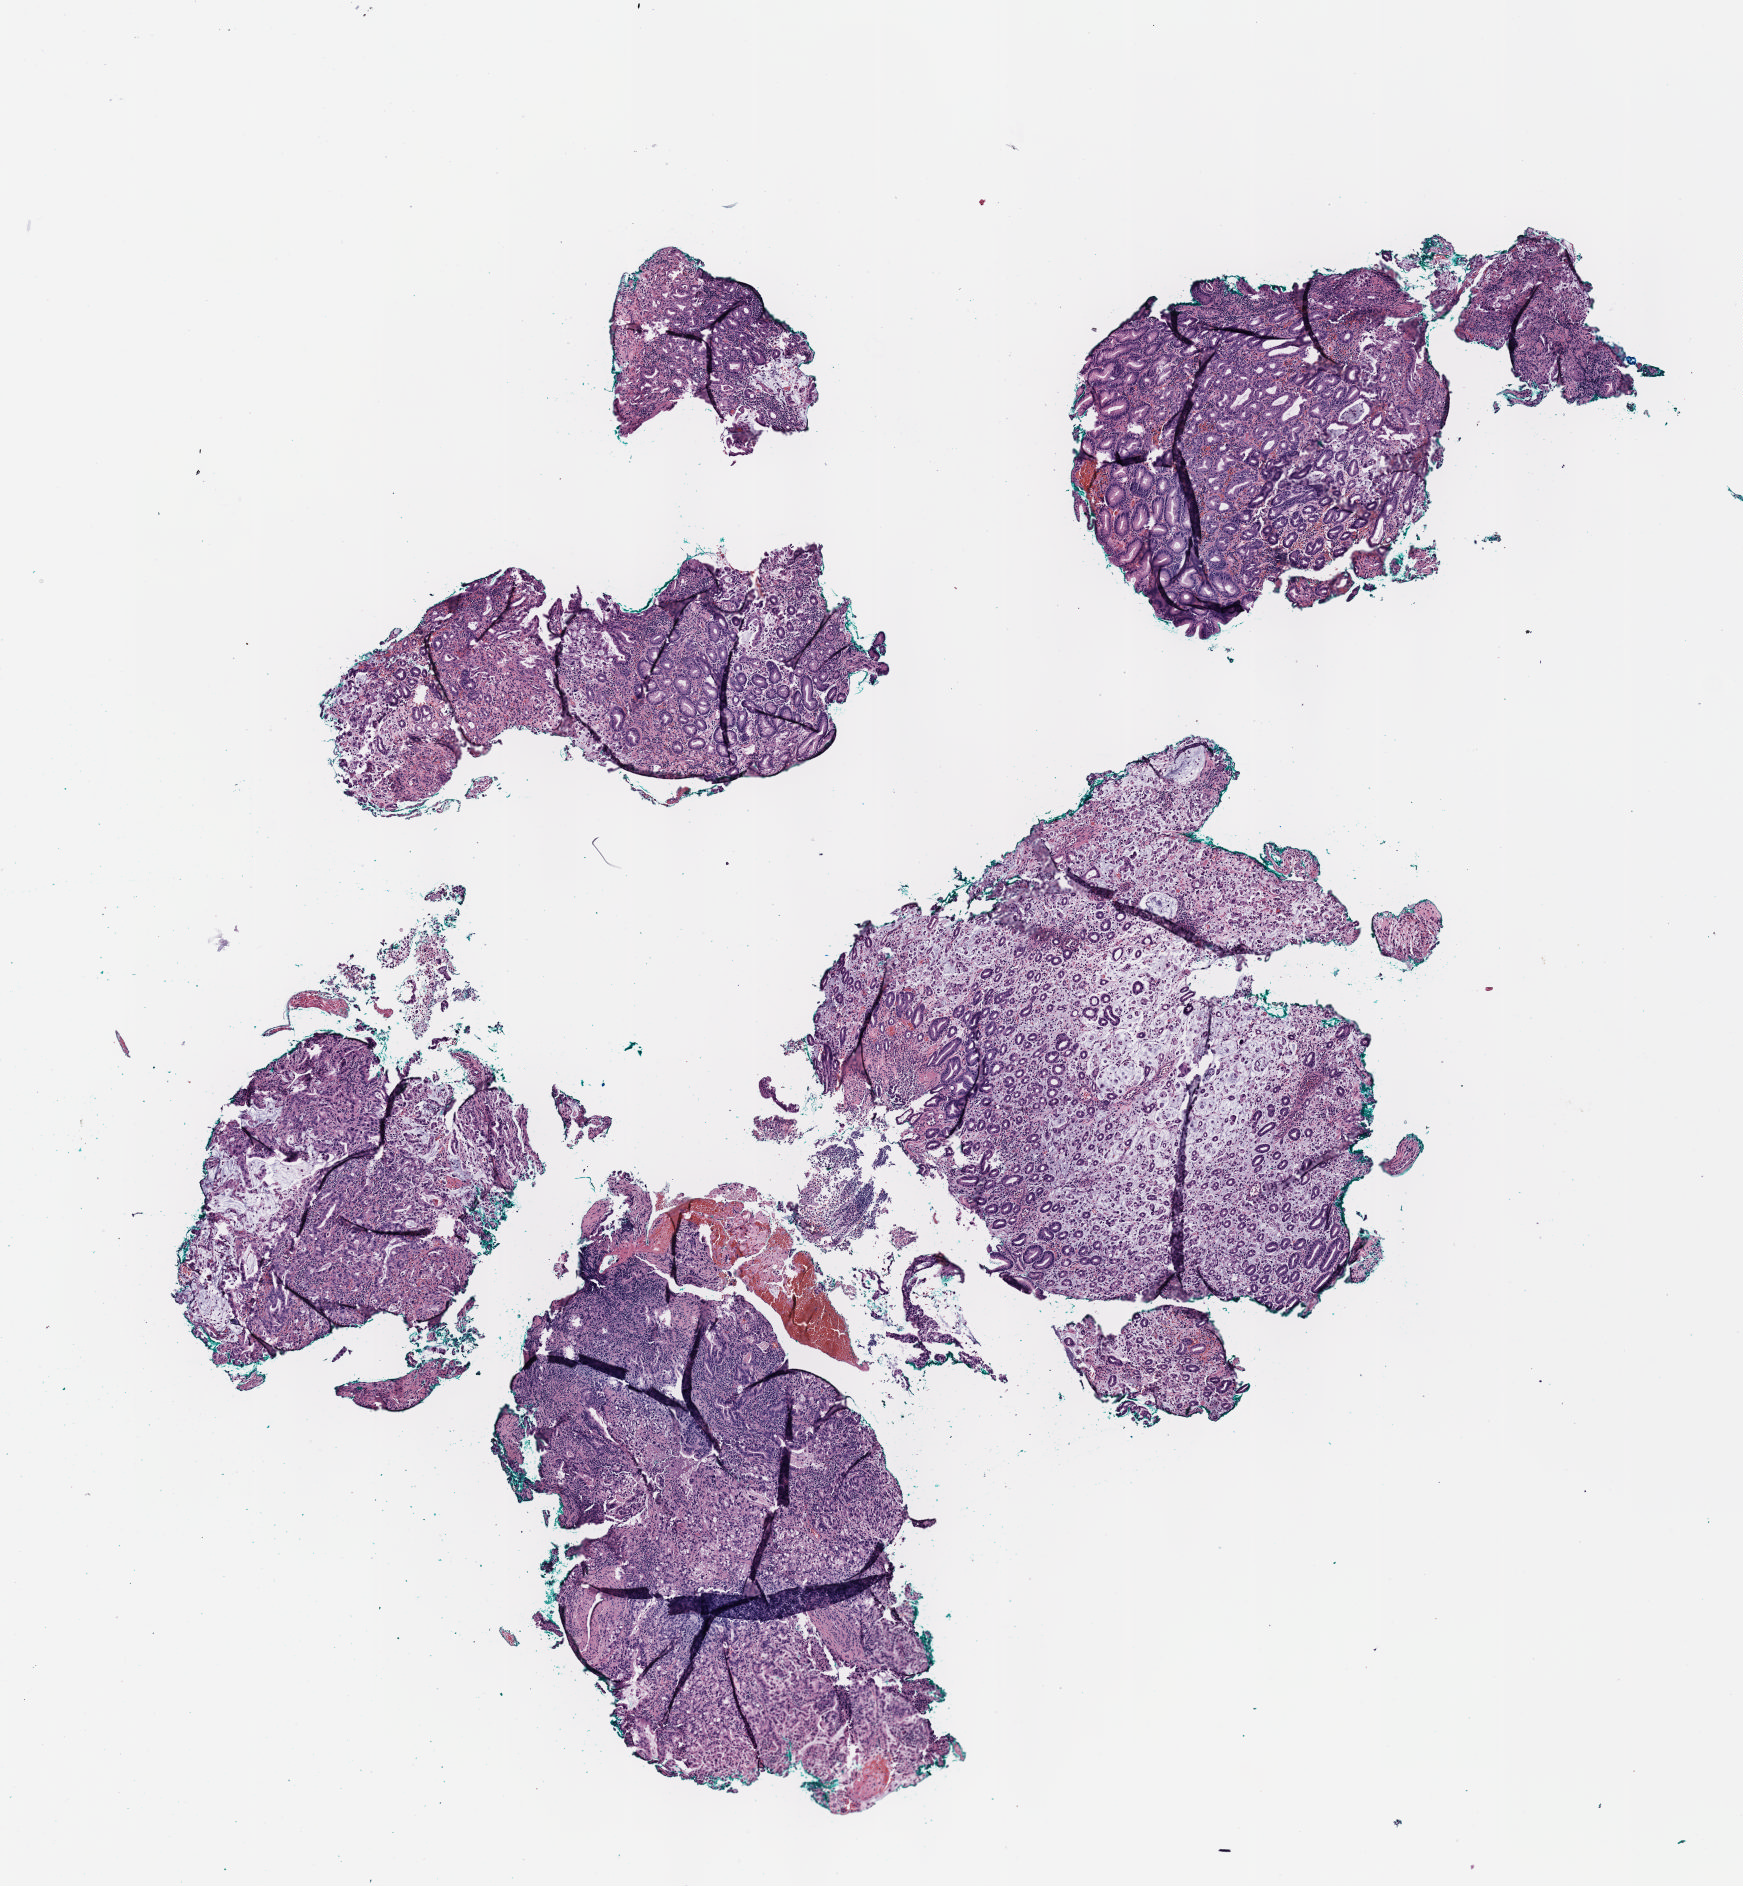
Digitized Hematoxylin and eosin (H&E) stained tissue section (whole slide), low-resolution overview of the scanned area, about 7.0 x 7.6 mm (from a 40x scan), formalin-fixed paraffin-embedded (FFPE) diagnostic section, sample: primary tumour, stomach. Patient: male, age at initial diagnosis 59 years. Histologic grade: G3 (poorly differentiated).
* AJCC pathologic stage: IIIC (6th edition)
* diagnosis: Signet ring cell carcinoma (cardia, NOS)